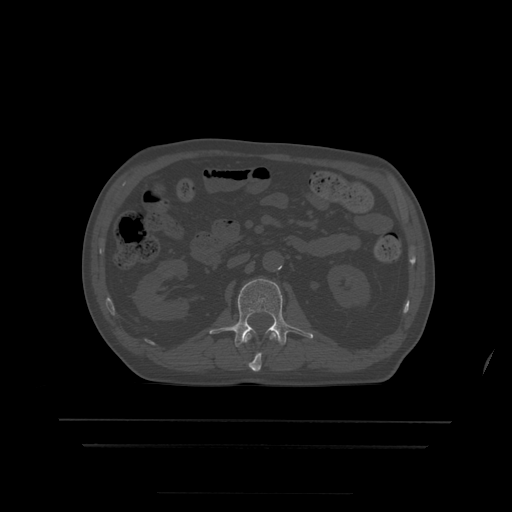
CT including the spine, one axial slice. Slice 151 of 522 in the series (ordered by position). Bone window (W 1800 / L 400 HU). 1.25 mm slice thickness. 512 × 512 image matrix. Patient age 68 years. From the clinical record (not read from this slice): primary cancer: urothelial.
Annotated regions visible in this slice (semi-automatic segmentation, software-assisted and operator-edited):
- L1 vertebra: bounding box (x1, y1, x2, y2) in pixels: (244, 333, 278, 372)
- L2 vertebra: (210, 279, 314, 347)